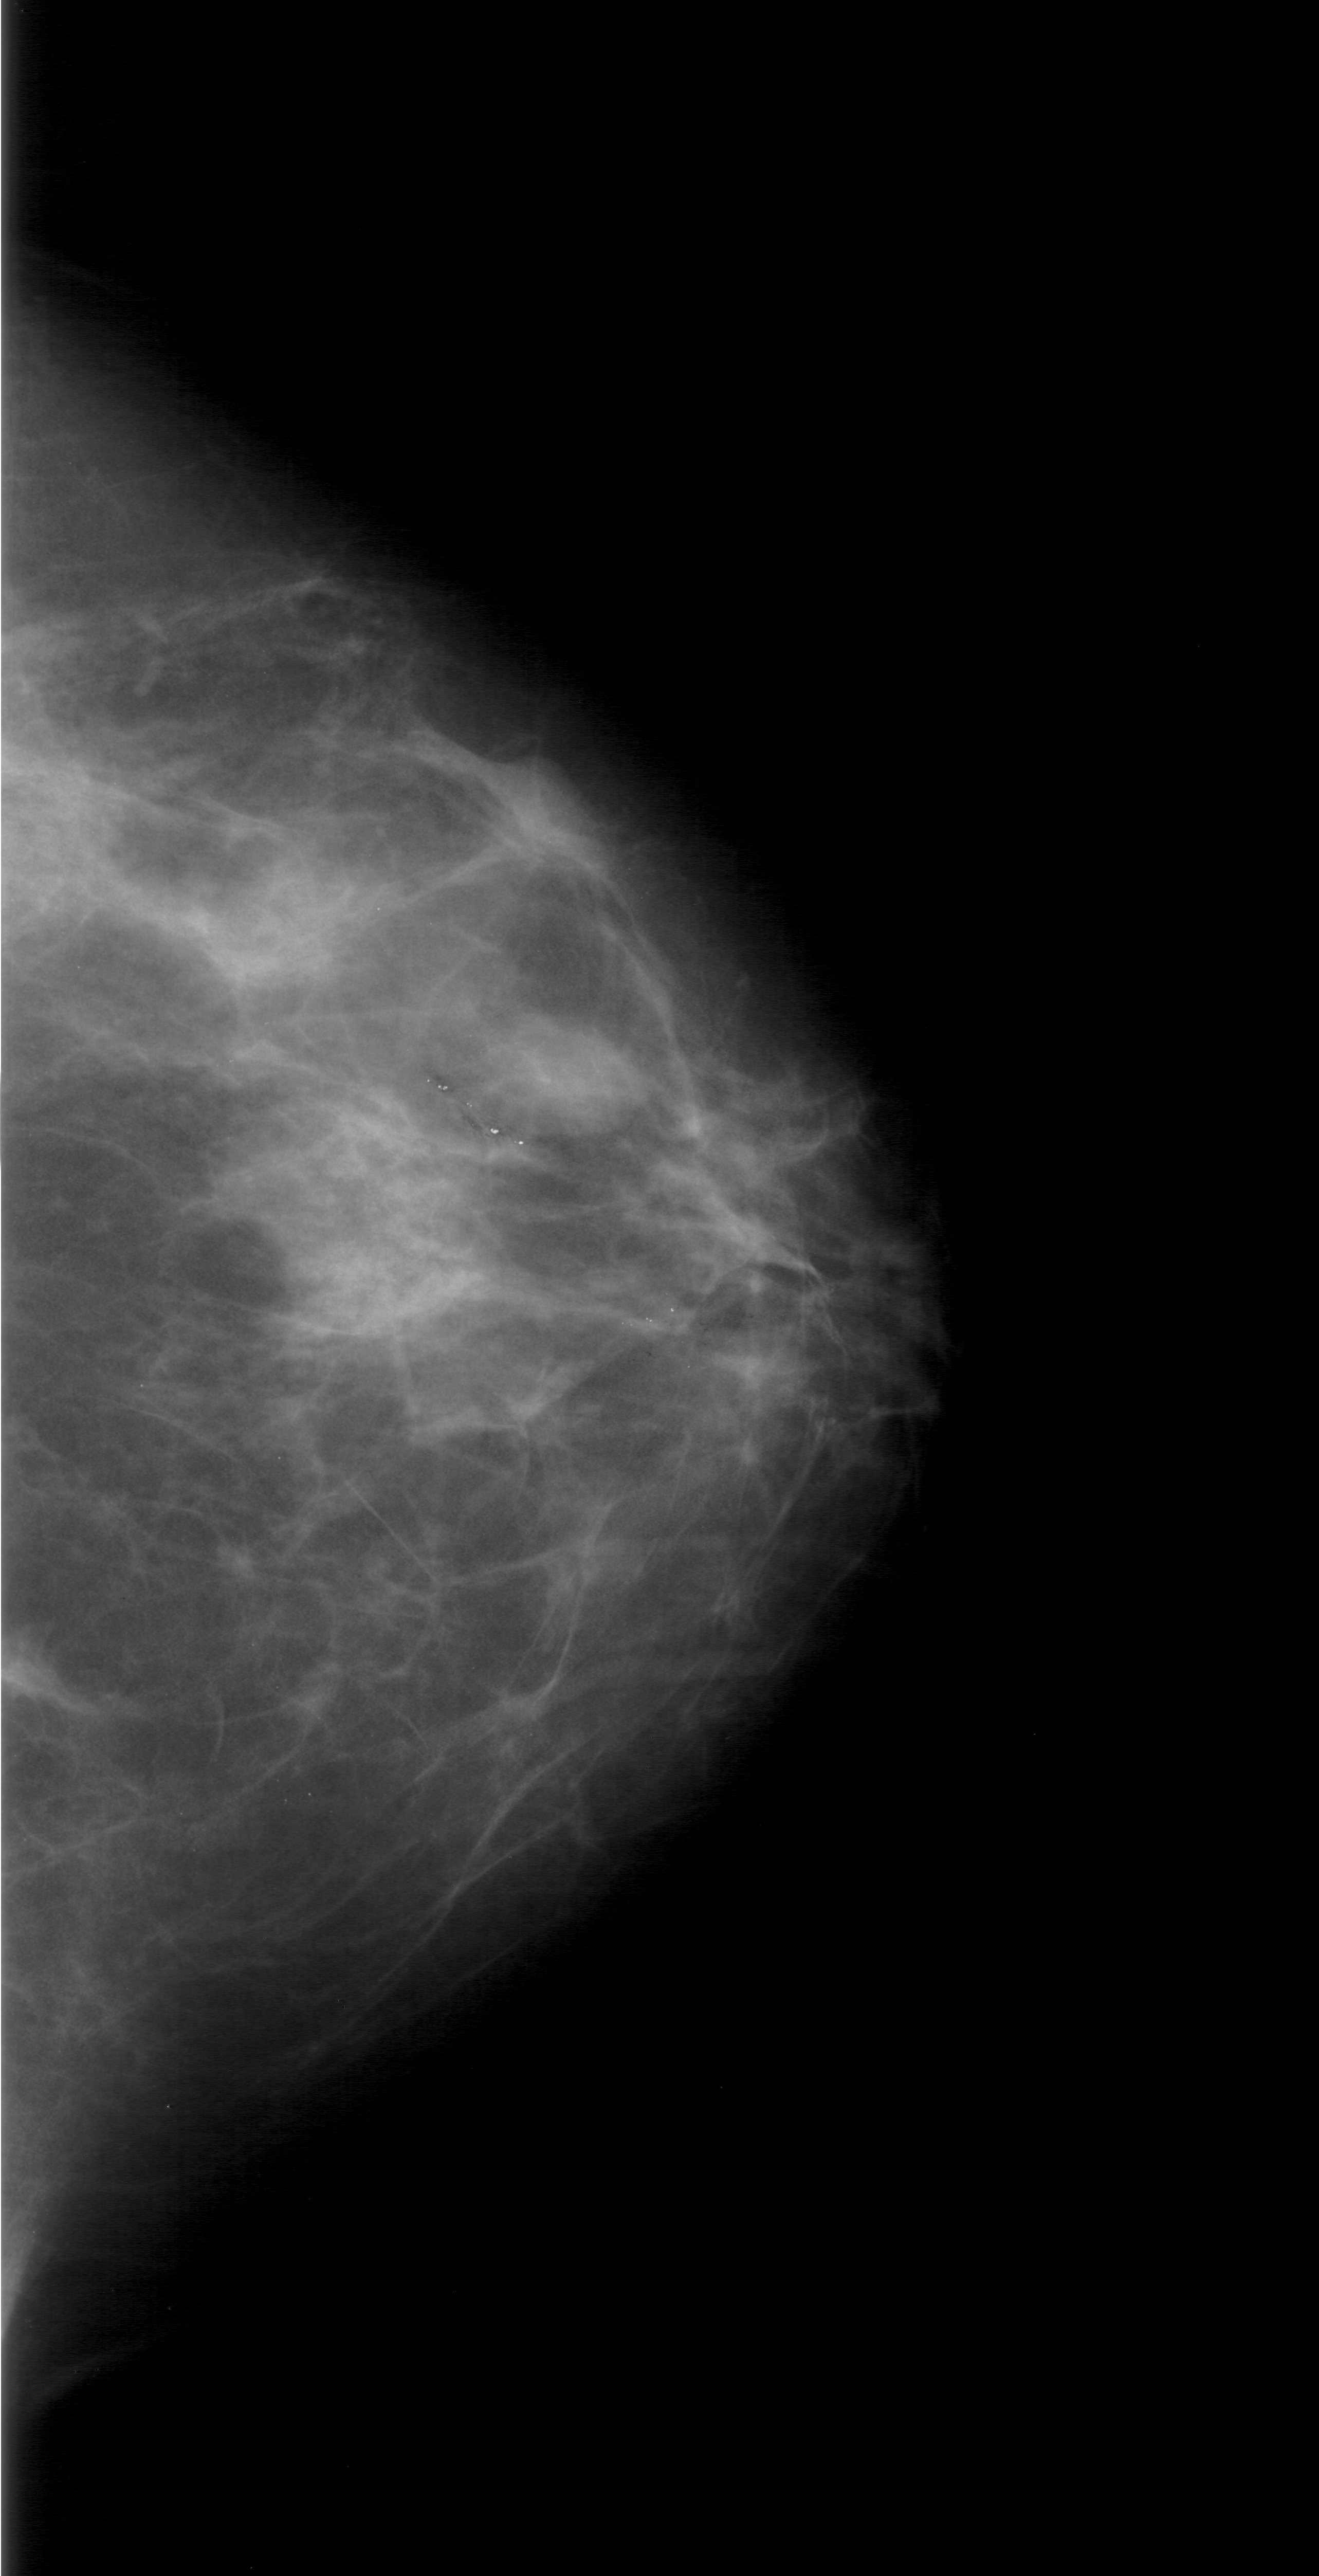
Scanned film-screen mammogram, right breast, CC view, breast composition: almost entirely fatty (BI-RADS density category 1 of 4).
- Marked findings (only marked abnormalities are described; nothing is implied about the rest of the image): mass, shape oval, margins obscured; BI-RADS assessment category 3; subtlety rating 3 on a 1 (subtle) to 5 (obvious) scale; pathology (as recorded): benign.